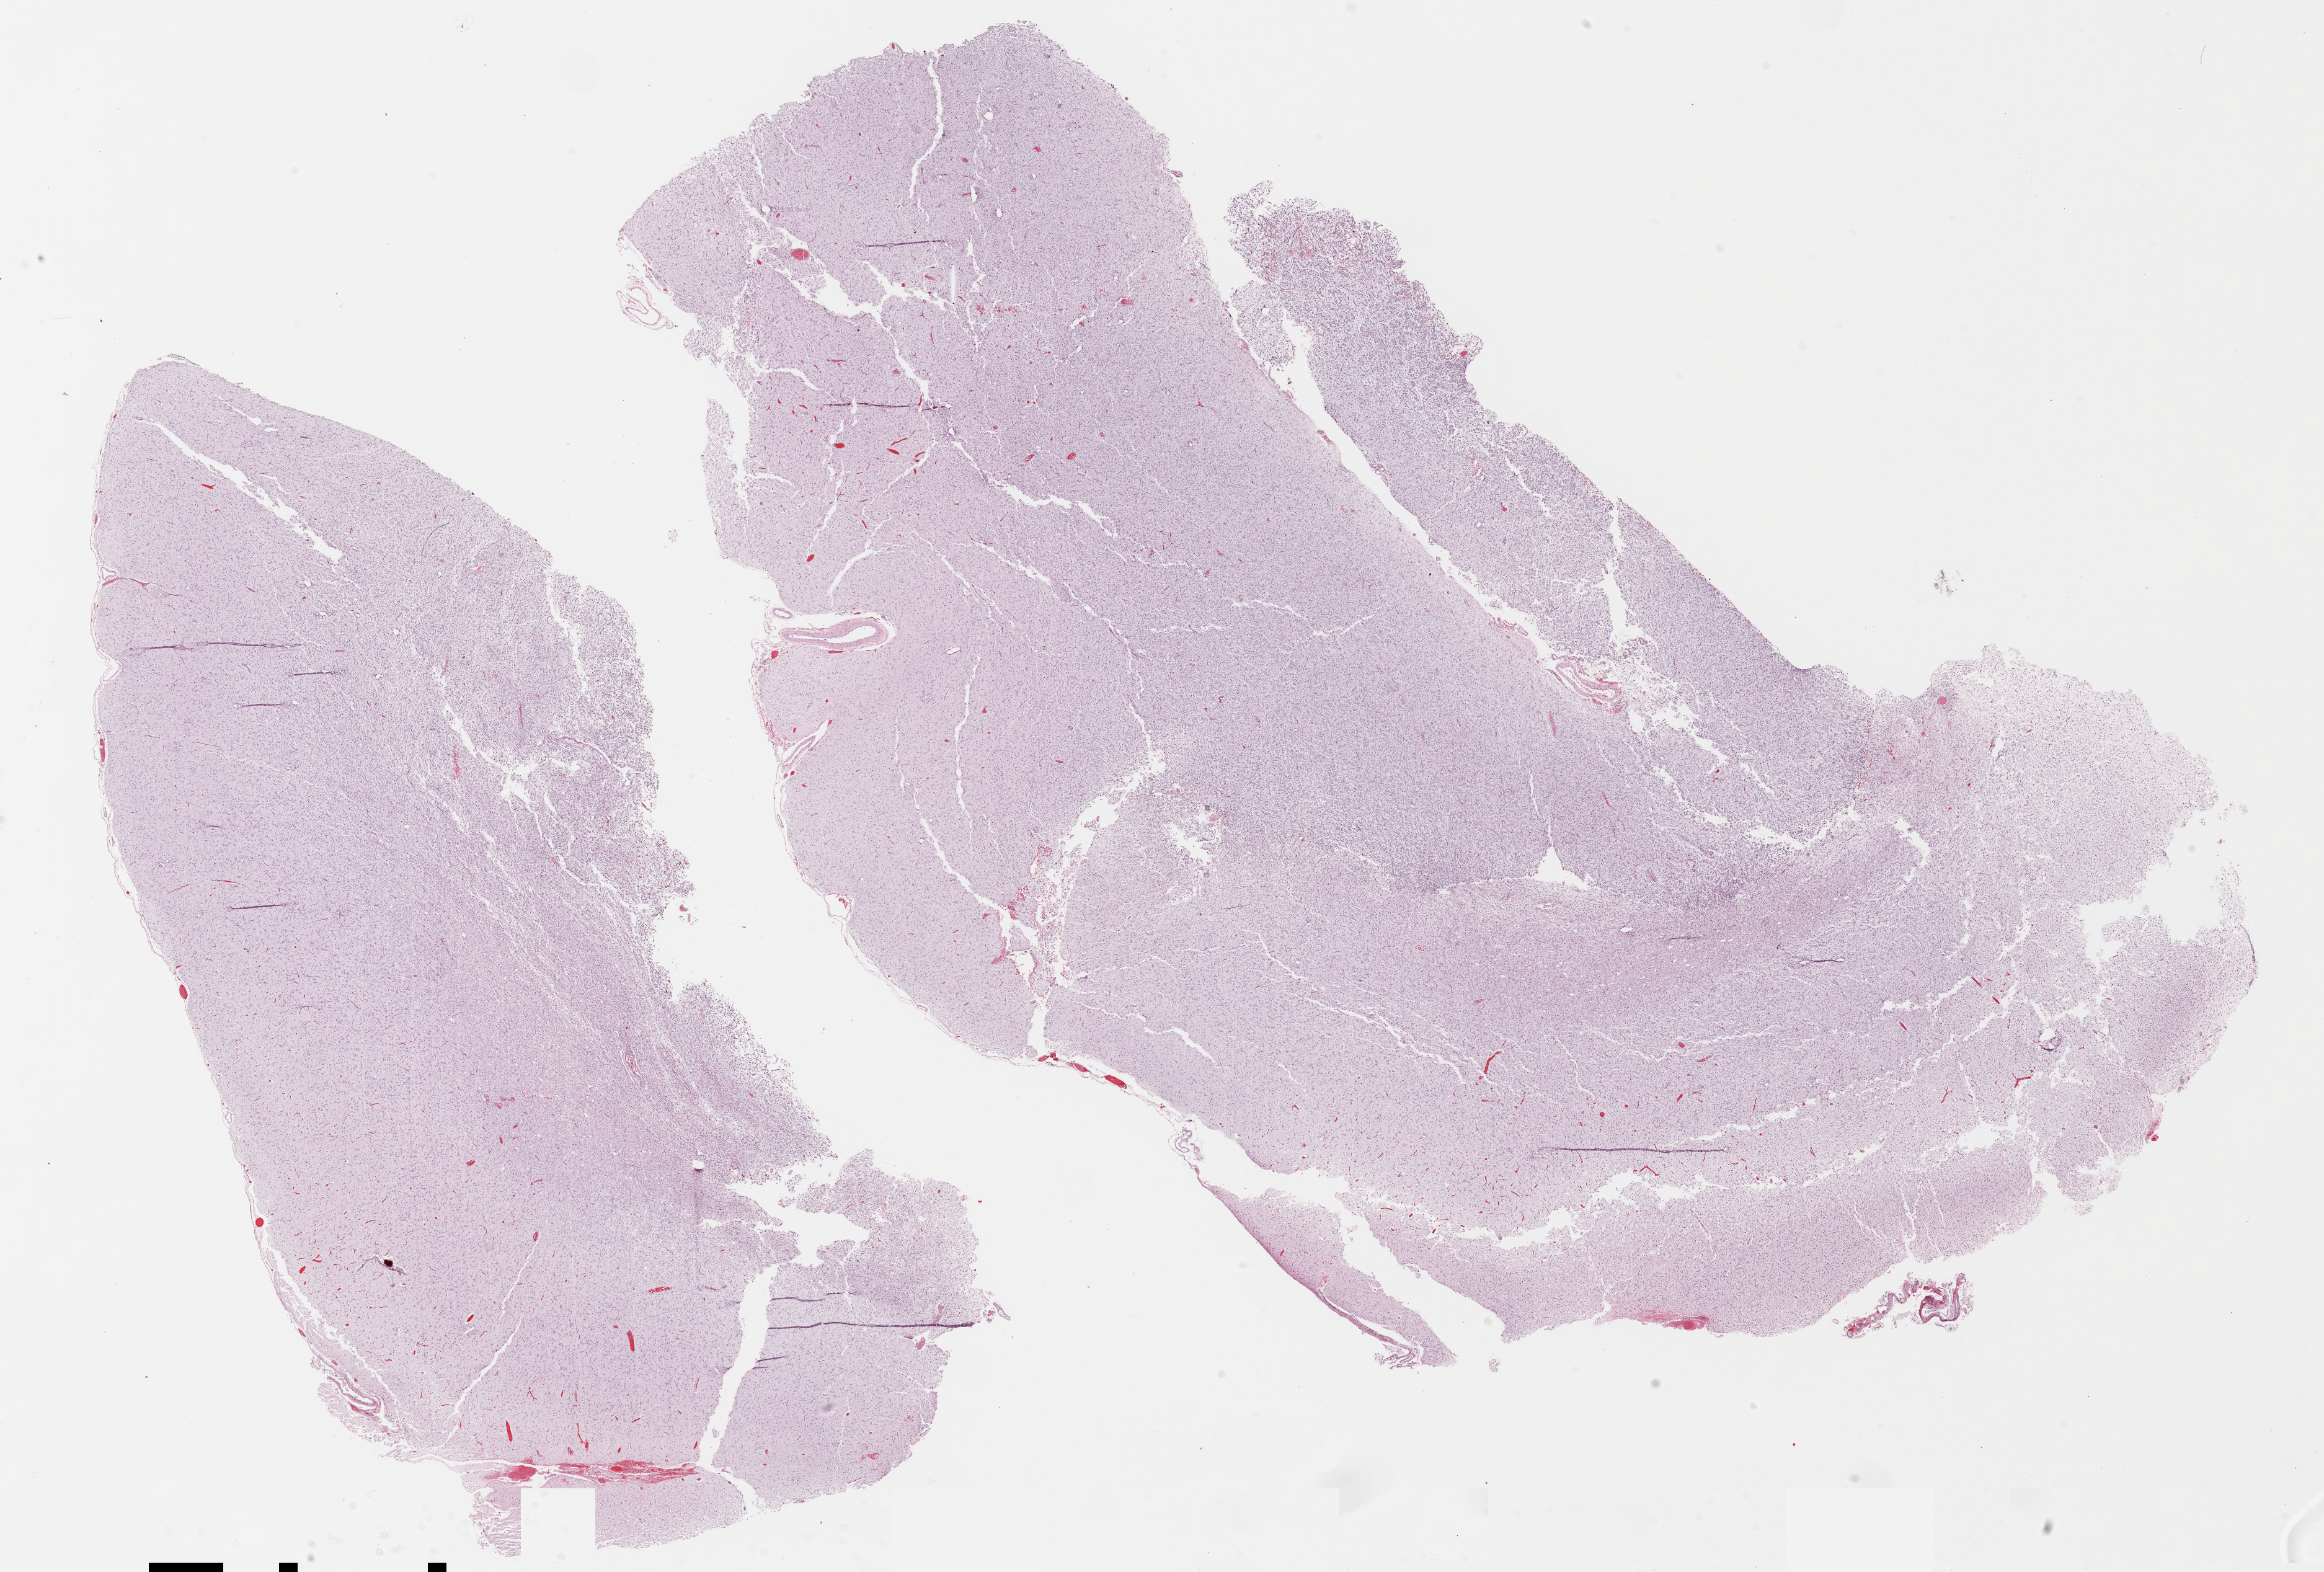
H&E whole-slide image — shown as a low-resolution overview of the whole scanned area (about 29.5 x 19.9 mm, acquisition: 40x scan). Formalin-fixed paraffin-embedded (FFPE) diagnostic section. Primary tumour sample from the brain. Male, age 31 years at initial diagnosis. Histologic grade: G3 (poorly differentiated).
Histologic diagnosis: Astrocytoma, NOS (cerebrum).